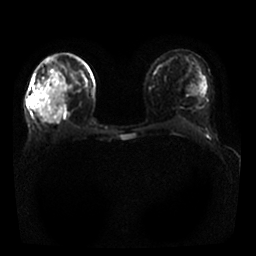
Breast MRI, one axial slice. Position 7 of 25 along the scan axis. Diffusion-weighted series; image 2 of 4 stored at this slice position (different b-values; order by instance number). 1.5 T. 256 × 256 image matrix, field of view 330 × 330 mm. Female patient.
Structures marked on this image (outlined manually by an expert reader):
- tumour on diffusion-weighted imaging: bounding box (x1, y1, x2, y2) in pixels: (29, 96, 37, 105)